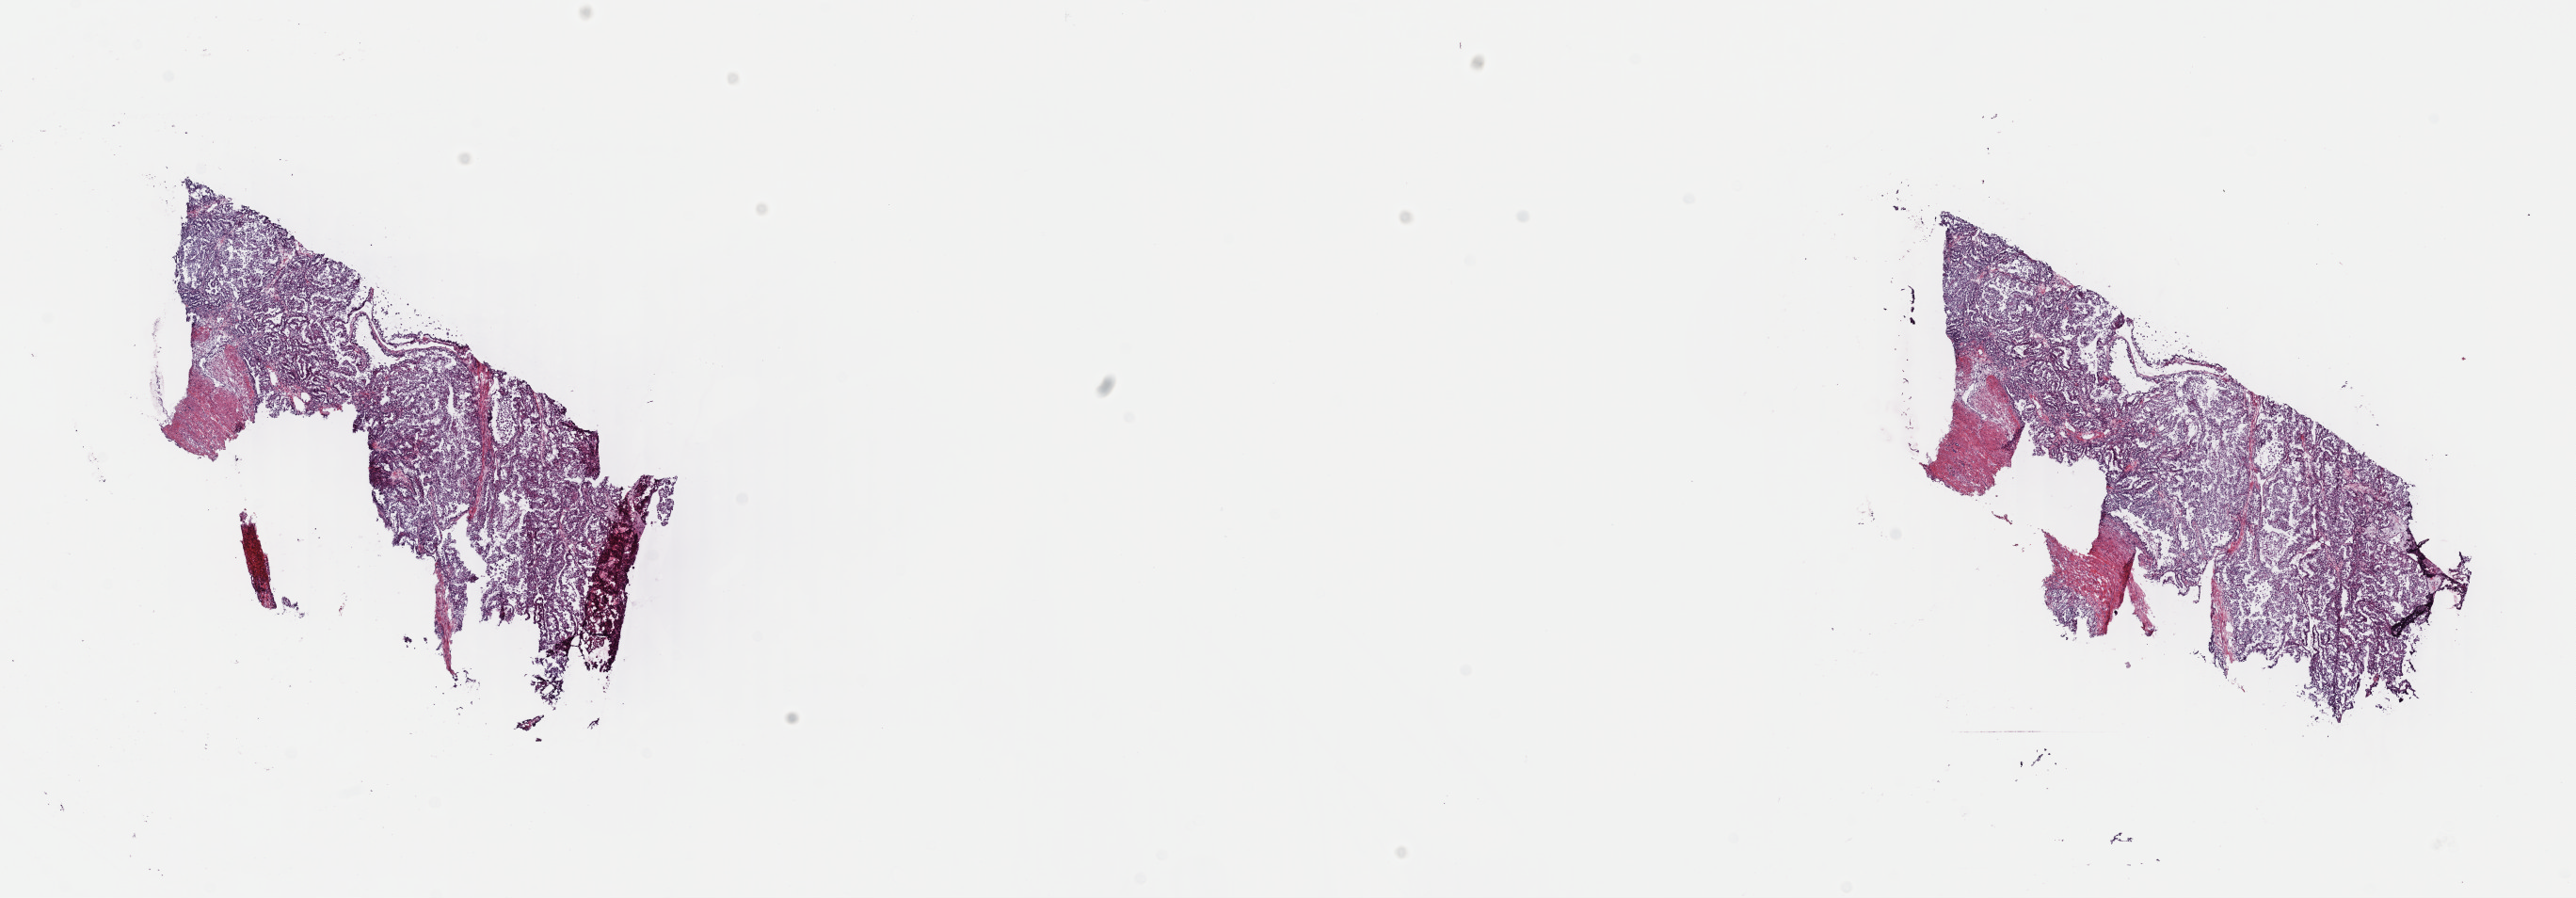
Hematoxylin and eosin (H&E) stained whole-slide image, shown as a low-resolution overview of the whole scanned area (about 21.6 x 7.5 mm, from a 40x scan). Frozen section. Sample: primary tumour, kidney. Male patient; age at initial diagnosis 41 years. Histologic grade: G2 (moderately differentiated). Pathologist review of this section (percent, as recorded): tumour cells 80%, tumour nuclei 90%, normal cells 0%, stromal cells 20%, necrosis 0%. Infiltration values recorded for this section: lymphocyte infiltration 0%, monocyte infiltration 100%, neutrophil infiltration 0%.
• pathologic diagnosis: Clear cell adenocarcinoma, NOS
• laterality: left